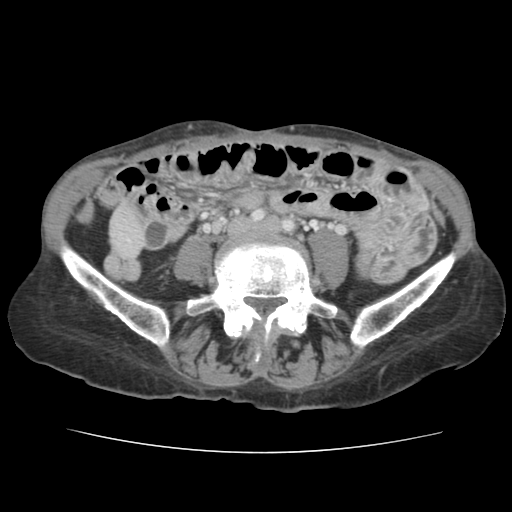
Contrast-enhanced abdominal CT, one axial slice; slice 10 of 136 in the series (ordered by position); 120 kVp; soft-tissue window (W 400 / L 40 HU); 2.5 mm slice thickness; 512 × 512 image matrix. Female patient, age 77 years. From the clinical record (not read from this slice): diagnosis: colorectal cancer liver metastases, imaged before liver resection; multiple liver metastases: yes; largest metastasis: 3 cm; disease in both lobes: no.
Structures marked on this image (manually delineated by an expert):
- liver: box from (x=112, y=209) to (x=143, y=256) px